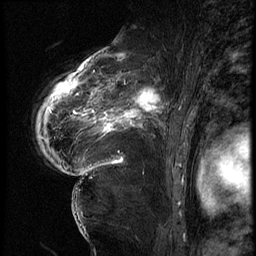
Breast MRI (dynamic contrast-enhanced), one sagittal slice. Position 45 of 62 along the scan axis. 3 images stored at this slice position (order not interpretable as contrast timing). 1.5 T. TE 4.2 ms, TR 9 ms. 256 × 256 image matrix, field of view 180 × 180 mm. Patient: female, 56 years. Case-level facts recorded for this patient, not image findings: setting: breast cancer imaged before/during neoadjuvant chemotherapy; receptor status: HER2-positive.
Outlined on this slice (semi-automatically segmented with operator editing):
- analysis volume of interest (the breast-tissue region the enhancement analysis was run in; not a lesion): box from (x=84, y=75) to (x=181, y=153) px
- tumour enhancement mask (voxels above the 140 % enhancement threshold inside the analysis volume of interest): (x=85, y=75)–(x=162, y=133)